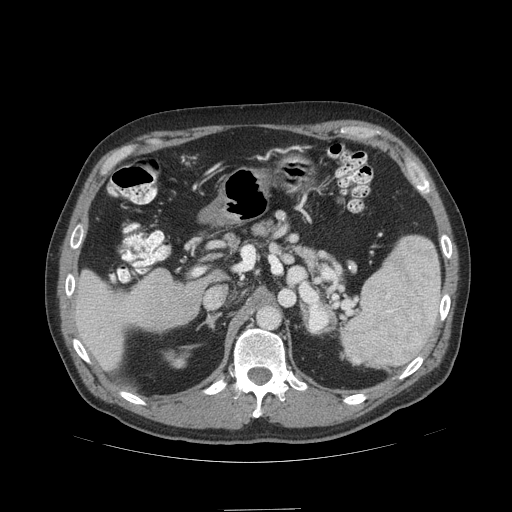
Contrast-enhanced abdominal CT (liver protocol), one axial slice. Slice 62 of 99 in the series (ordered by position). Reconstruction kernel STANDARD. Soft-tissue window (W 400 / L 40 HU). 2.5 mm slice thickness. 512 × 512 image matrix, field of view 440 × 440 mm. From the clinical record (not read from this slice): diagnosis: hepatocellular carcinoma (patient treated with transarterial chemoembolisation; whether this scan precedes or follows treatment is not stated here); TNM stage (as recorded): Stage-I.
Structures marked on this image (semi-automatically segmented with operator editing):
- liver parenchyma outside the tumour (the mass and vessels are separate outlines, so this box may not span the whole liver): bounding box <72,270,164,370> (left, top, right, bottom; pixels)